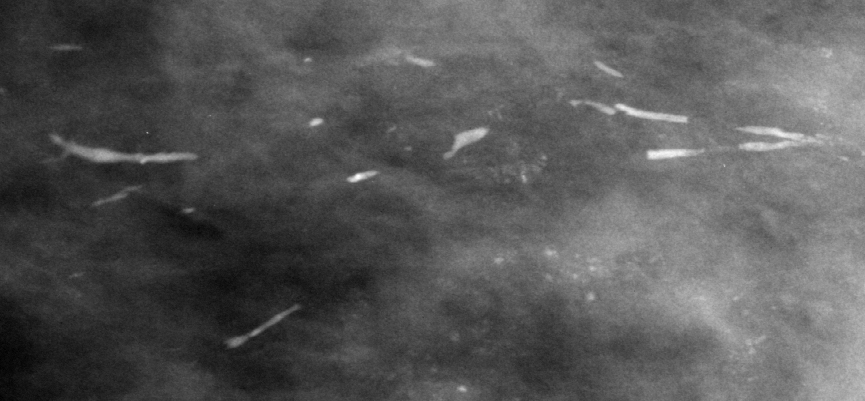
Cropped region of a digitized screen-film mammogram centred on a radiologist-marked abnormality; left breast; CC view.
Marked abnormality: calcifications, morphology punctate / lucent center, distribution regional; BI-RADS assessment category 2; benign without callback (not worked up further).